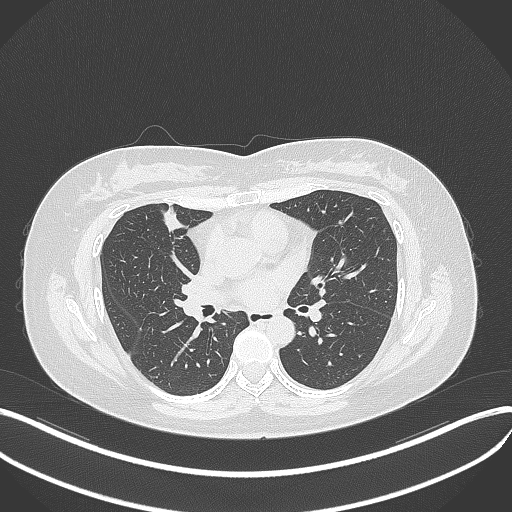
Chest CT, one axial slice. Slice 165 of 273 in the series (ordered by position). Reconstruction kernel B70f. Lung window (W 1500 / L -600 HU). 512 × 512 image matrix, field of view 400 × 400 mm. Patient: female, 42 years. Case-level facts recorded for this patient, not image findings: clinical TNM (as recorded): T1b N0 M0.
Outlined on this slice (bounding box drawn by a radiologist):
- lung tumour (recorded histology: adenocarcinoma): box from (x=157, y=200) to (x=193, y=236) px